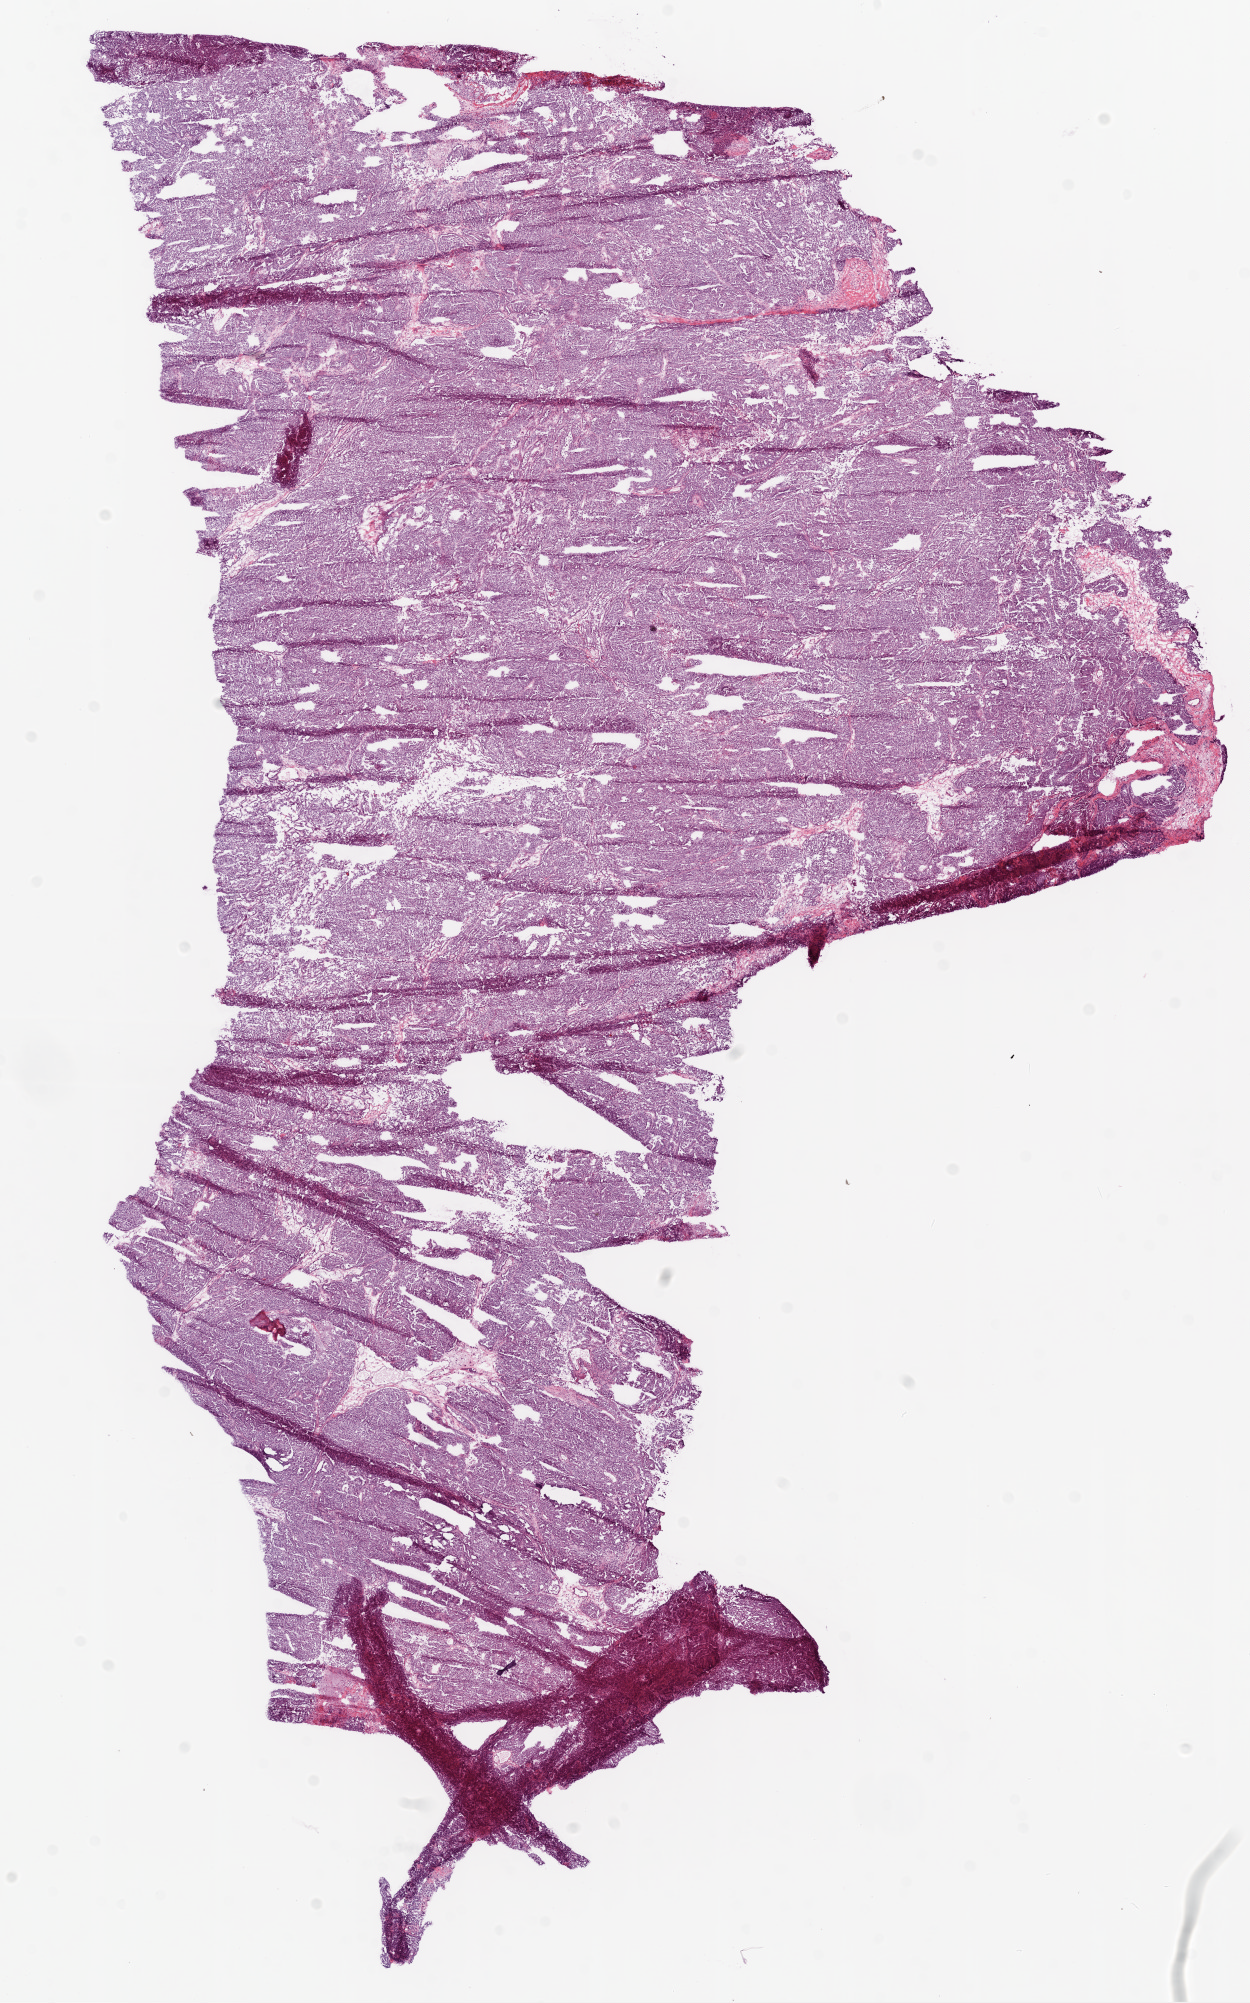
Whole-slide histology image, H&E-stained, a low-resolution overview of the entire scanned area, about 10.0 x 16.1 mm, frozen section from the bottom of the tissue portion, sample: primary tumour, ovary. Female, age 59 years at initial diagnosis. Slide review estimates, as recorded: tumour cells 94%, tumour nuclei 95%.
Histologic diagnosis: Serous cystadenocarcinoma, NOS.